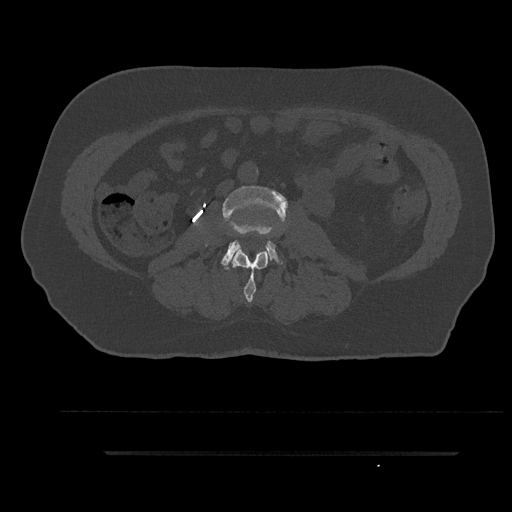
CT including the spine, one axial slice; position 73 of 797 along the scan axis; bone window (W 1800 / L 400 HU); 512 × 512 image matrix, field of view 432 × 432 mm. Male patient, age 63 years. Case-level facts recorded for this patient, not image findings: primary cancer: renal; vertebrae with lytic lesions (as recorded): T8.
Outlined on this slice (semi-automatic segmentation, software-assisted and operator-edited):
- L2 vertebra: bounding box [x1, y1, x2, y2] px = [232, 250, 268, 302]
- L3 vertebra: [222, 185, 288, 269]